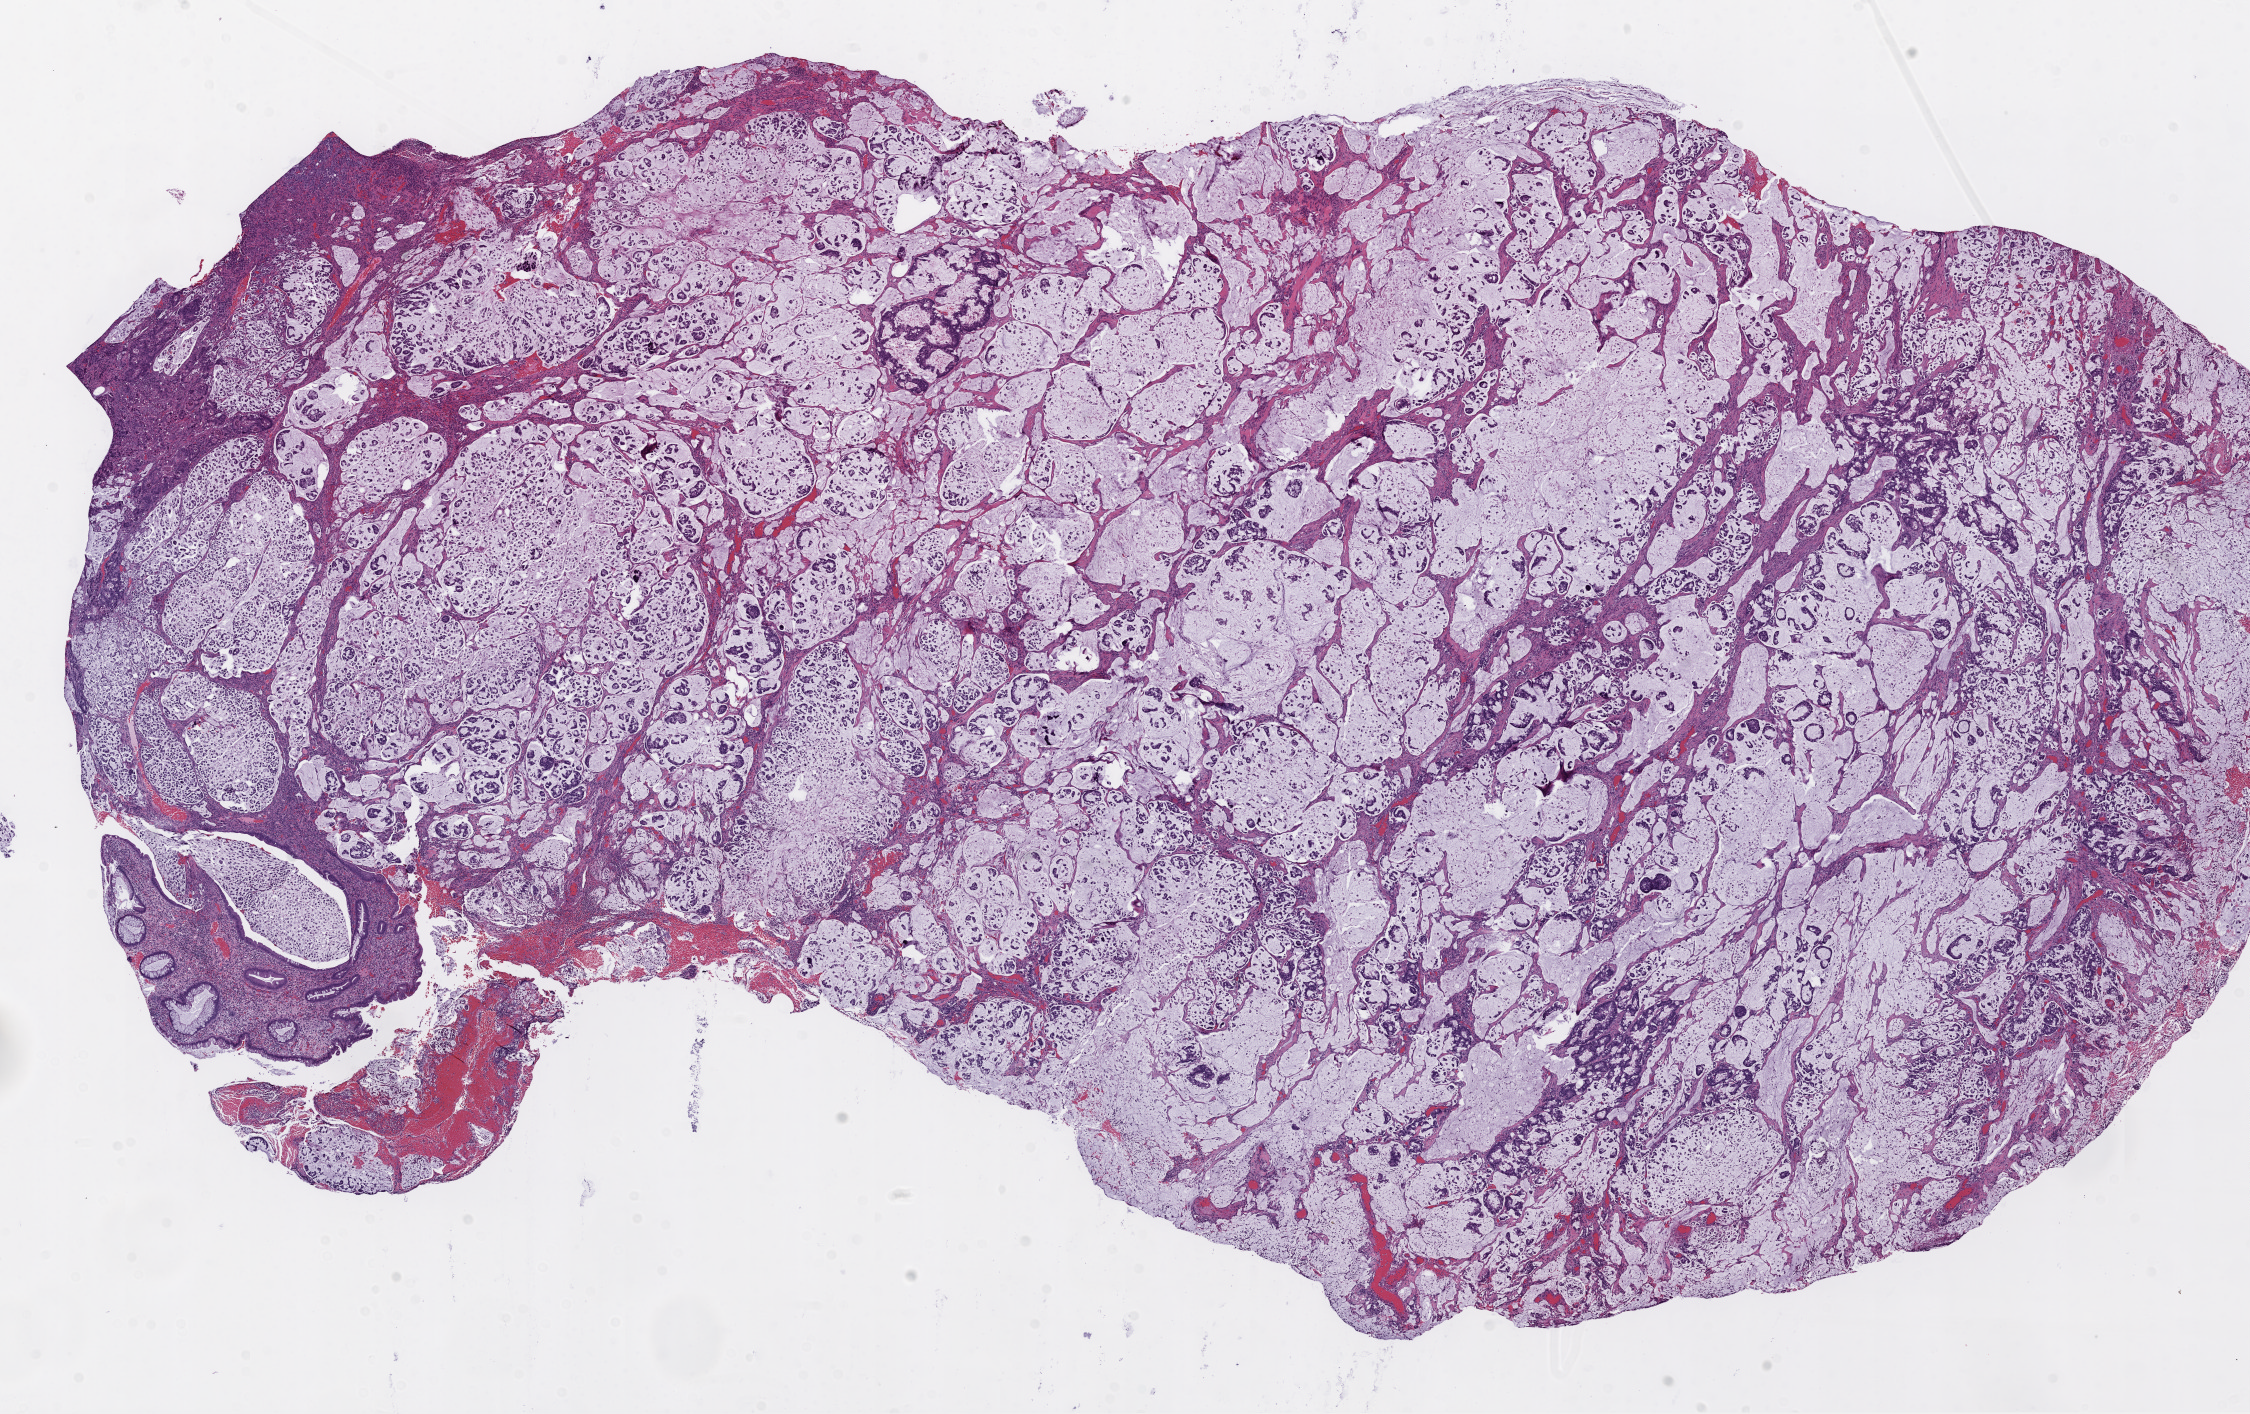
Whole-slide histology image, H&E-stained — low-resolution overview of the scanned area, about 18.1 x 11.3 mm (from a 20x scan); frozen section from the top of the tissue portion; primary tumour sample from the rectum. Patient: male, age at initial diagnosis 54 years. Composition of this section per pathologist review: tumour cells 90%, tumour nuclei 80%, normal cells 3%, stromal cells 7%, necrosis 0%.
Histologic diagnosis: Mucinous adenocarcinoma. Lymph nodes positive (case pathology): 0 of 32 examined. AJCC pathologic stage: IIA.